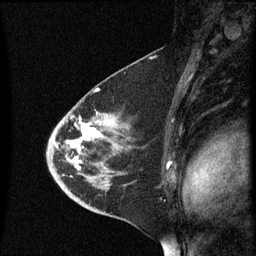
Breast MRI (dynamic contrast-enhanced), one sagittal slice; position 37 of 60 along the scan axis; dynamic contrast-enhanced series, image 2 of 3 at this slice position (ordered by acquisition); 1.5 T; TE 4.2 ms, TR 8.4 ms; 2.3 mm slice thickness; 256 × 256 image matrix, field of view 200 × 200 mm. Patient: female, 46 years. From the clinical record (not read from this slice): setting: breast cancer imaged before/during neoadjuvant chemotherapy; receptor status: HER2-positive.
Structures marked on this image (semi-automatic segmentation, software-assisted and operator-edited):
- analysis volume of interest (the breast-tissue region the enhancement analysis was run in; not a lesion): bounding box <47,96,134,187> (left, top, right, bottom; pixels)
- tumour enhancement mask (voxels above the 70 % enhancement threshold inside the analysis volume of interest): <55,118,113,169>